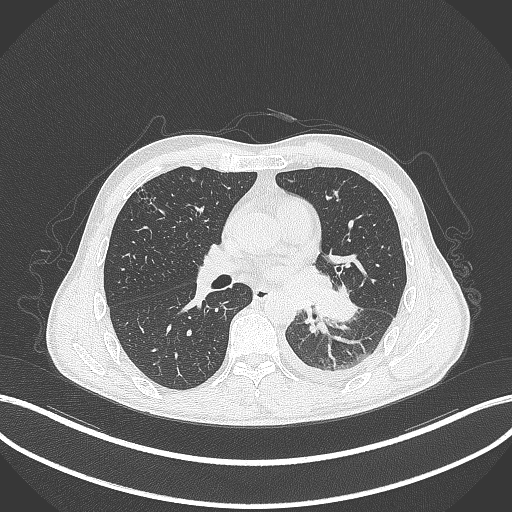
Chest CT, one axial slice. Position 165 of 295 along the scan axis. Reconstruction kernel B70f. 120 kVp. Lung window (W 1500 / L -600 HU). 512 × 512 image matrix, field of view 400 × 400 mm. Patient: male, 47 years. From the clinical record (not read from this slice): clinical TNM (as recorded): T3 N1 M1c.
Annotated regions visible in this slice (bounding box drawn by a radiologist):
- lung tumour (recorded histology: small cell carcinoma): bounding box <313,281,365,326> (left, top, right, bottom; pixels)